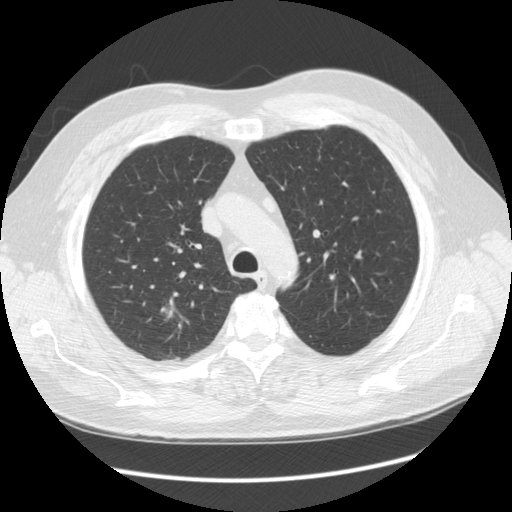
Low-dose screening chest CT, one axial slice; position 81 of 108 along the scan axis; reconstruction kernel STANDARD; lung window (W 1500 / L -600 HU); 2.5 mm slice thickness; 512 × 512 image matrix, field of view 380 × 380 mm.
Outlined on this slice (manually delineated by an expert):
- lesion 1 (tumor, upper lobe of right lung): bounding box [x1, y1, x2, y2] px = [161, 307, 175, 318]